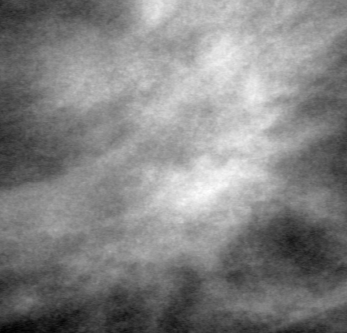
Cropped region of a digitized screen-film mammogram centred on a radiologist-marked abnormality; left breast; MLO view.
Mass, shape architectural distortion, margins spiculated; BI-RADS assessment category 5; pathology result (as recorded, not read from the image): malignant.